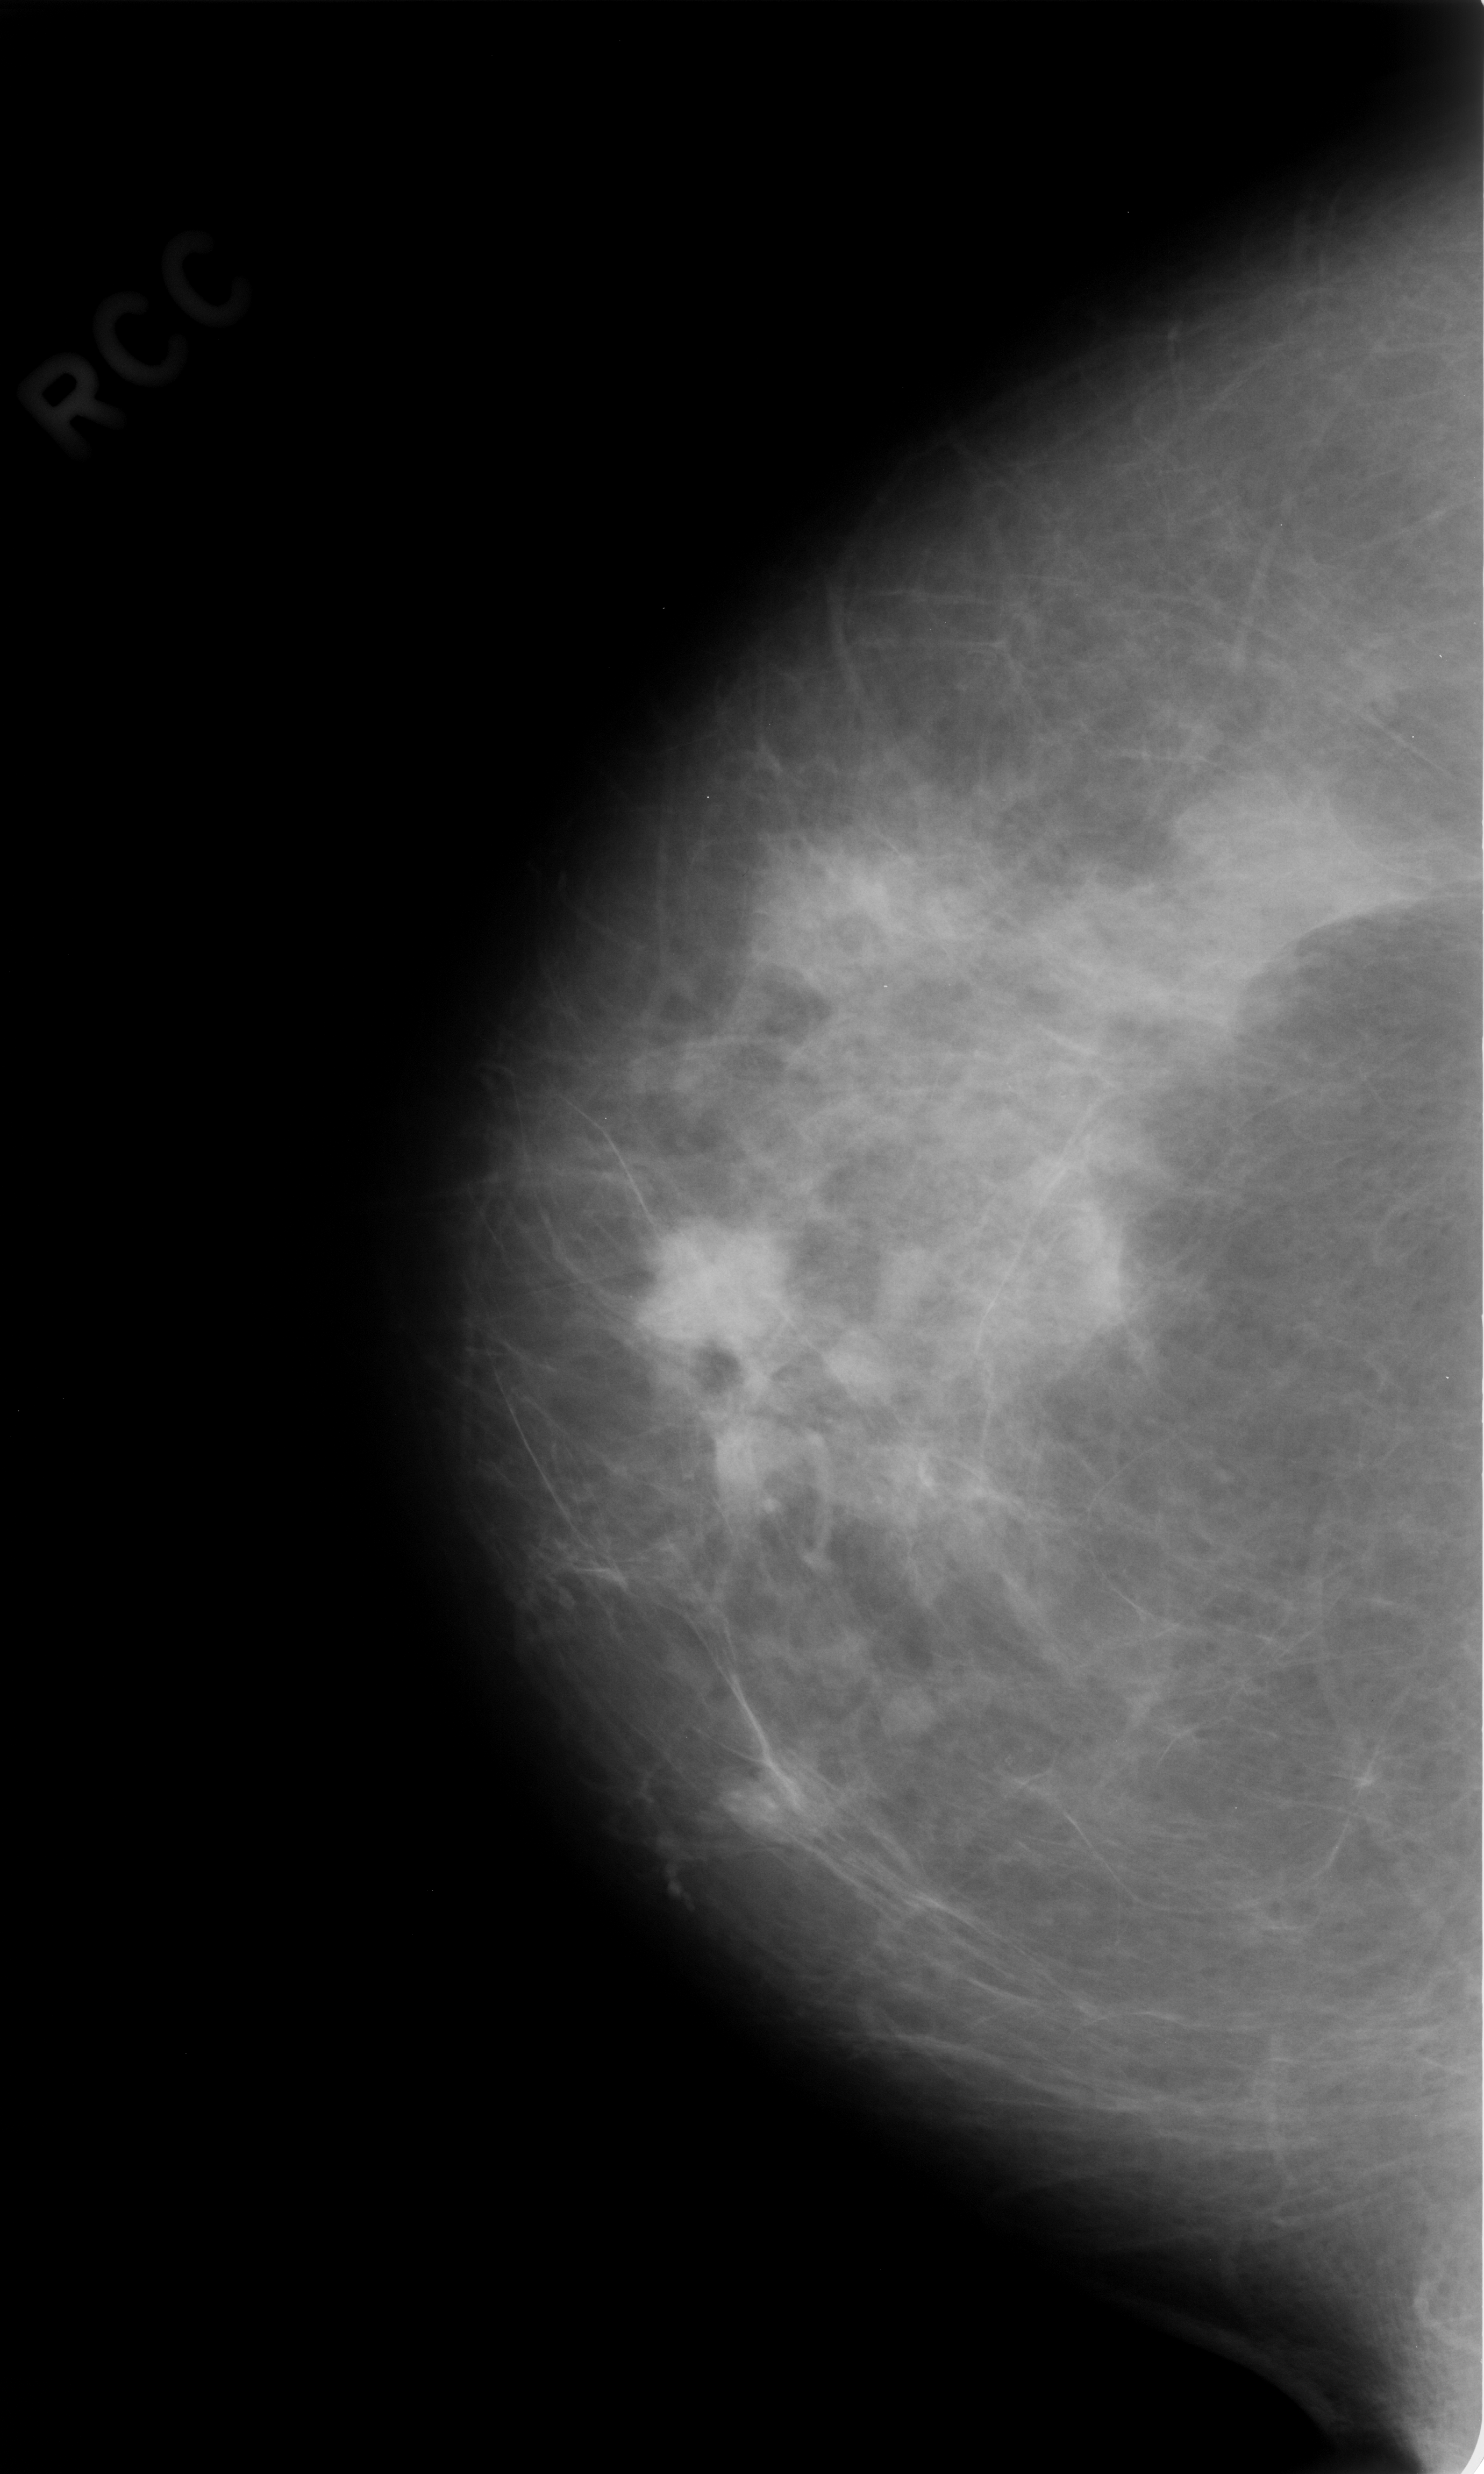
Digitized screen-film mammogram. Right breast. CC view. 1484 × 2474 image matrix.
Expert-marked regions of interest on this image (one box per marked abnormality):
- mass, shape lobulated, margins circumscribed; BI-RADS assessment category 4; subtlety rating 5 on a 1 (subtle) to 5 (obvious) scale; pathology result (as recorded, not read from the image): benign: bounding box <617,1201,793,1365> (left, top, right, bottom; pixels)